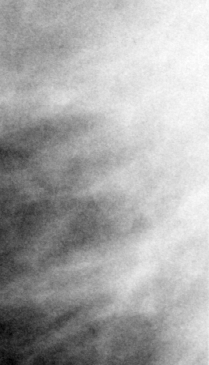
Region of interest cut from a scanned film mammogram (one marked finding), right breast, MLO view, BI-RADS breast density category 2 (scale 1–4).
Finding: mass, shape irregular, margins spiculated; BI-RADS assessment category 5; subtlety rating 5 on a 1 (subtle) to 5 (obvious) scale; pathology (as recorded): malignant.